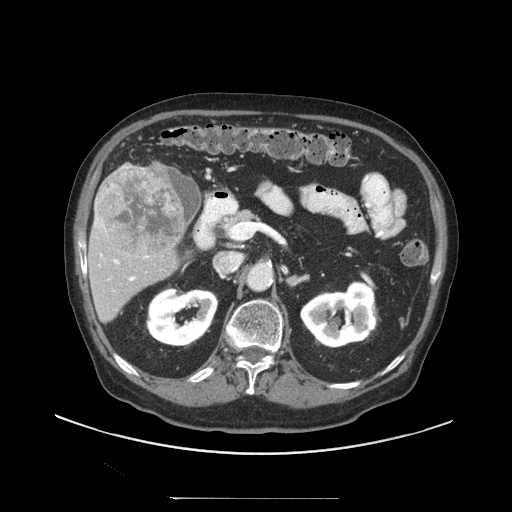
Contrast-enhanced abdominal CT (liver protocol), one axial slice; position 49 of 97 along the scan axis; reconstruction kernel STANDARD; 140 kVp; soft-tissue window (W 400 / L 40 HU); 2.5 mm slice thickness; 512 × 512 image matrix, field of view 450 × 450 mm. Case-level facts recorded for this patient, not image findings: diagnosis: hepatocellular carcinoma (patient treated with transarterial chemoembolisation; whether this scan precedes or follows treatment is not stated here); TNM stage (as recorded): Stage-IIIC; Child-Pugh class: A; tumour differentiation: well differentiated.
Structures marked on this image (semi-automatically segmented with operator editing):
- liver parenchyma outside the tumour (the mass and vessels are separate outlines, so this box may not span the whole liver): bounding box (x1, y1, x2, y2) in pixels: (88, 162, 187, 322)
- mass: (98, 166, 185, 258)
- liver vessels: (94, 207, 135, 281)